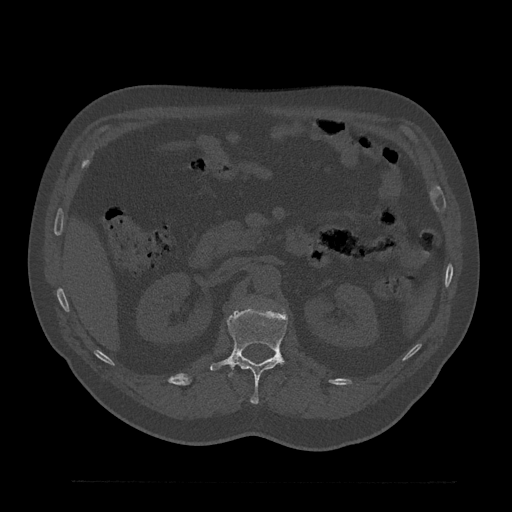
CT including the spine, one axial slice. Position 160 of 797 along the scan axis. Reconstruction kernel Br40s/3. Bone window (W 1800 / L 400 HU). 512 × 512 image matrix, field of view 430 × 430 mm. Patient: male, 61 years. From the clinical record (not read from this slice): primary cancer: prostate.
Annotated regions visible in this slice (semi-automatically segmented with operator editing):
- L1 vertebra: bounding box <210,307,288,404> (left, top, right, bottom; pixels)